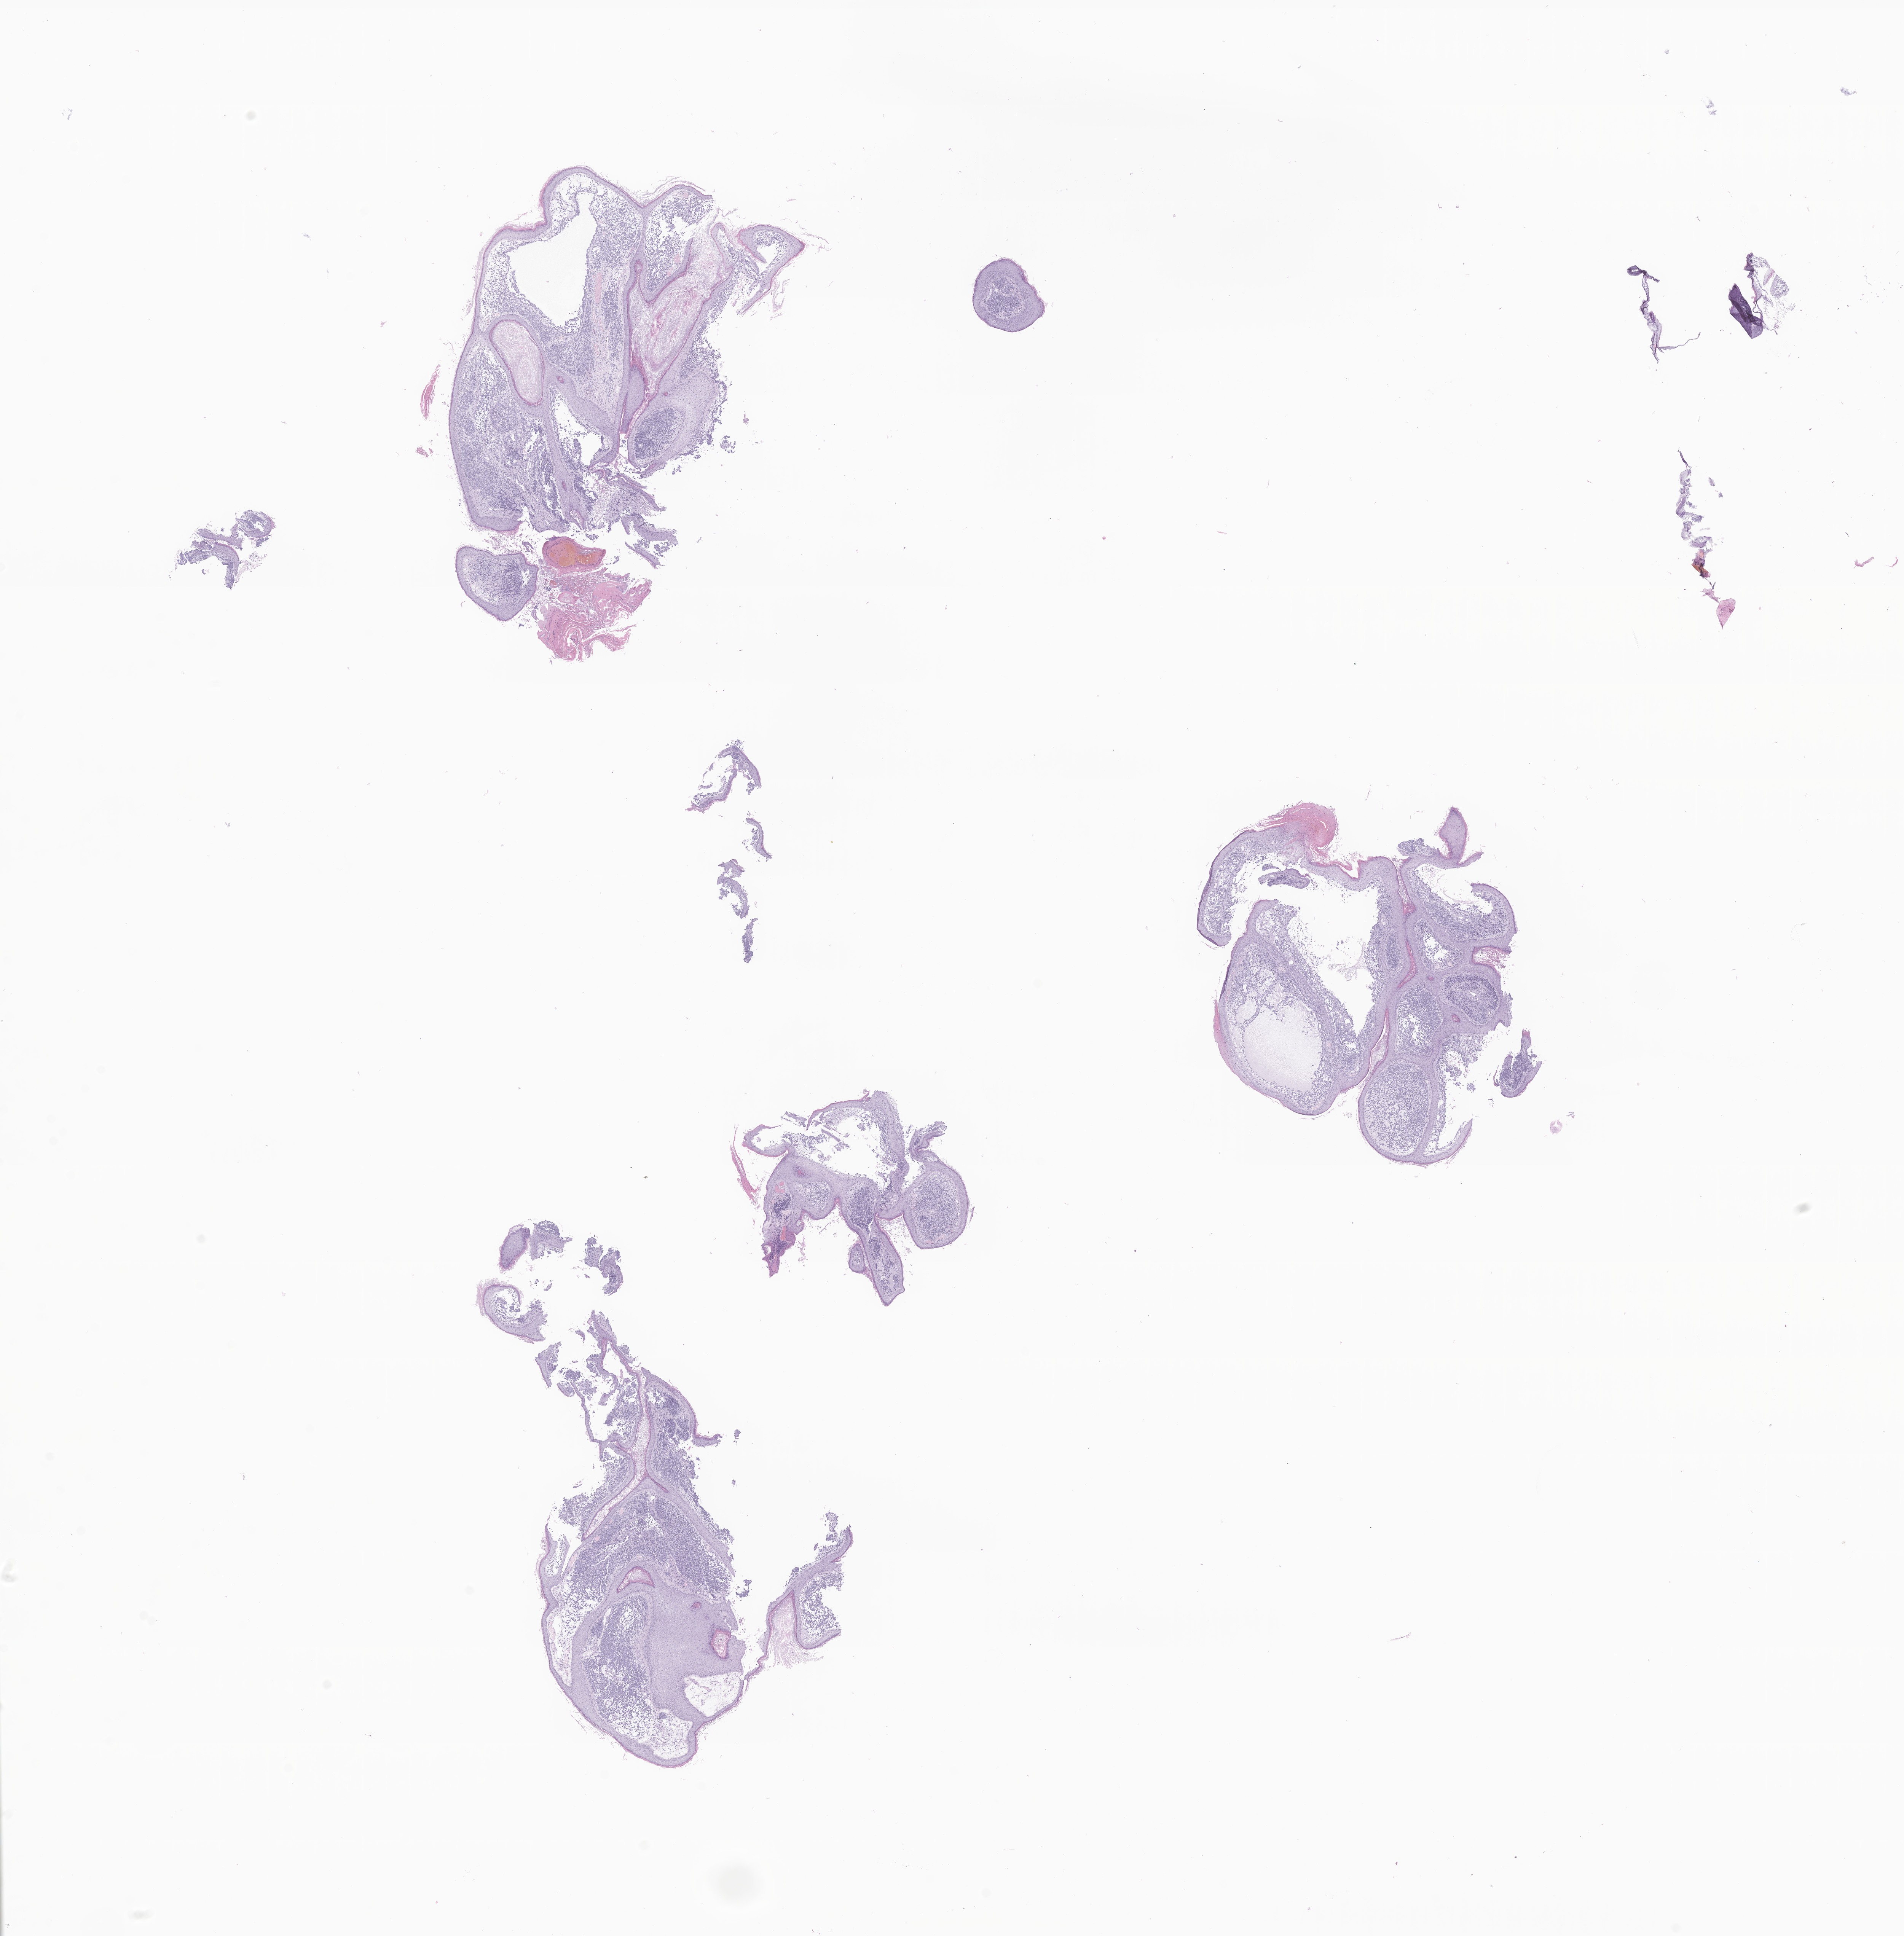
Whole-slide image, haematoxylin and eosin stain of tumor tissue from the external ear — whole scanned area (about 21.1 x 21.4 mm) shown as a low-resolution overview, FFPE section. Patient: male, age 907 days.
Recorded diagnosis: Embryonal rhabdomyosarcoma, NOS.